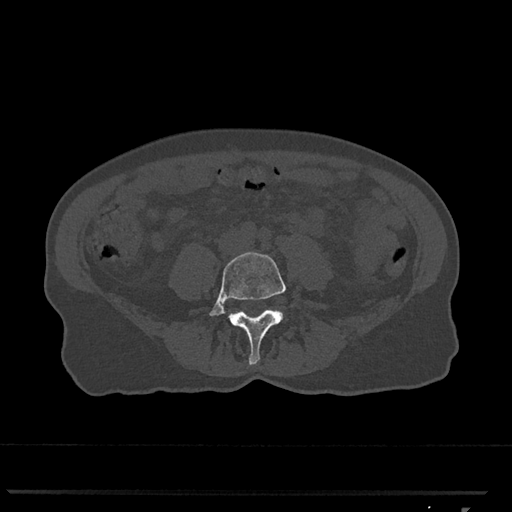
CT including the spine, one axial slice; position 204 of 793 along the scan axis; reconstruction kernel Br40s/3; 120 kVp; bone window (W 1800 / L 400 HU); 0.5 mm slice thickness; 512 × 512 image matrix. Female patient, age 62 years. From the clinical record (not read from this slice): primary cancer: renal.
Annotated regions visible in this slice (semi-automatically segmented with operator editing):
- L4 vertebra: bounding box <209,252,293,365> (left, top, right, bottom; pixels)